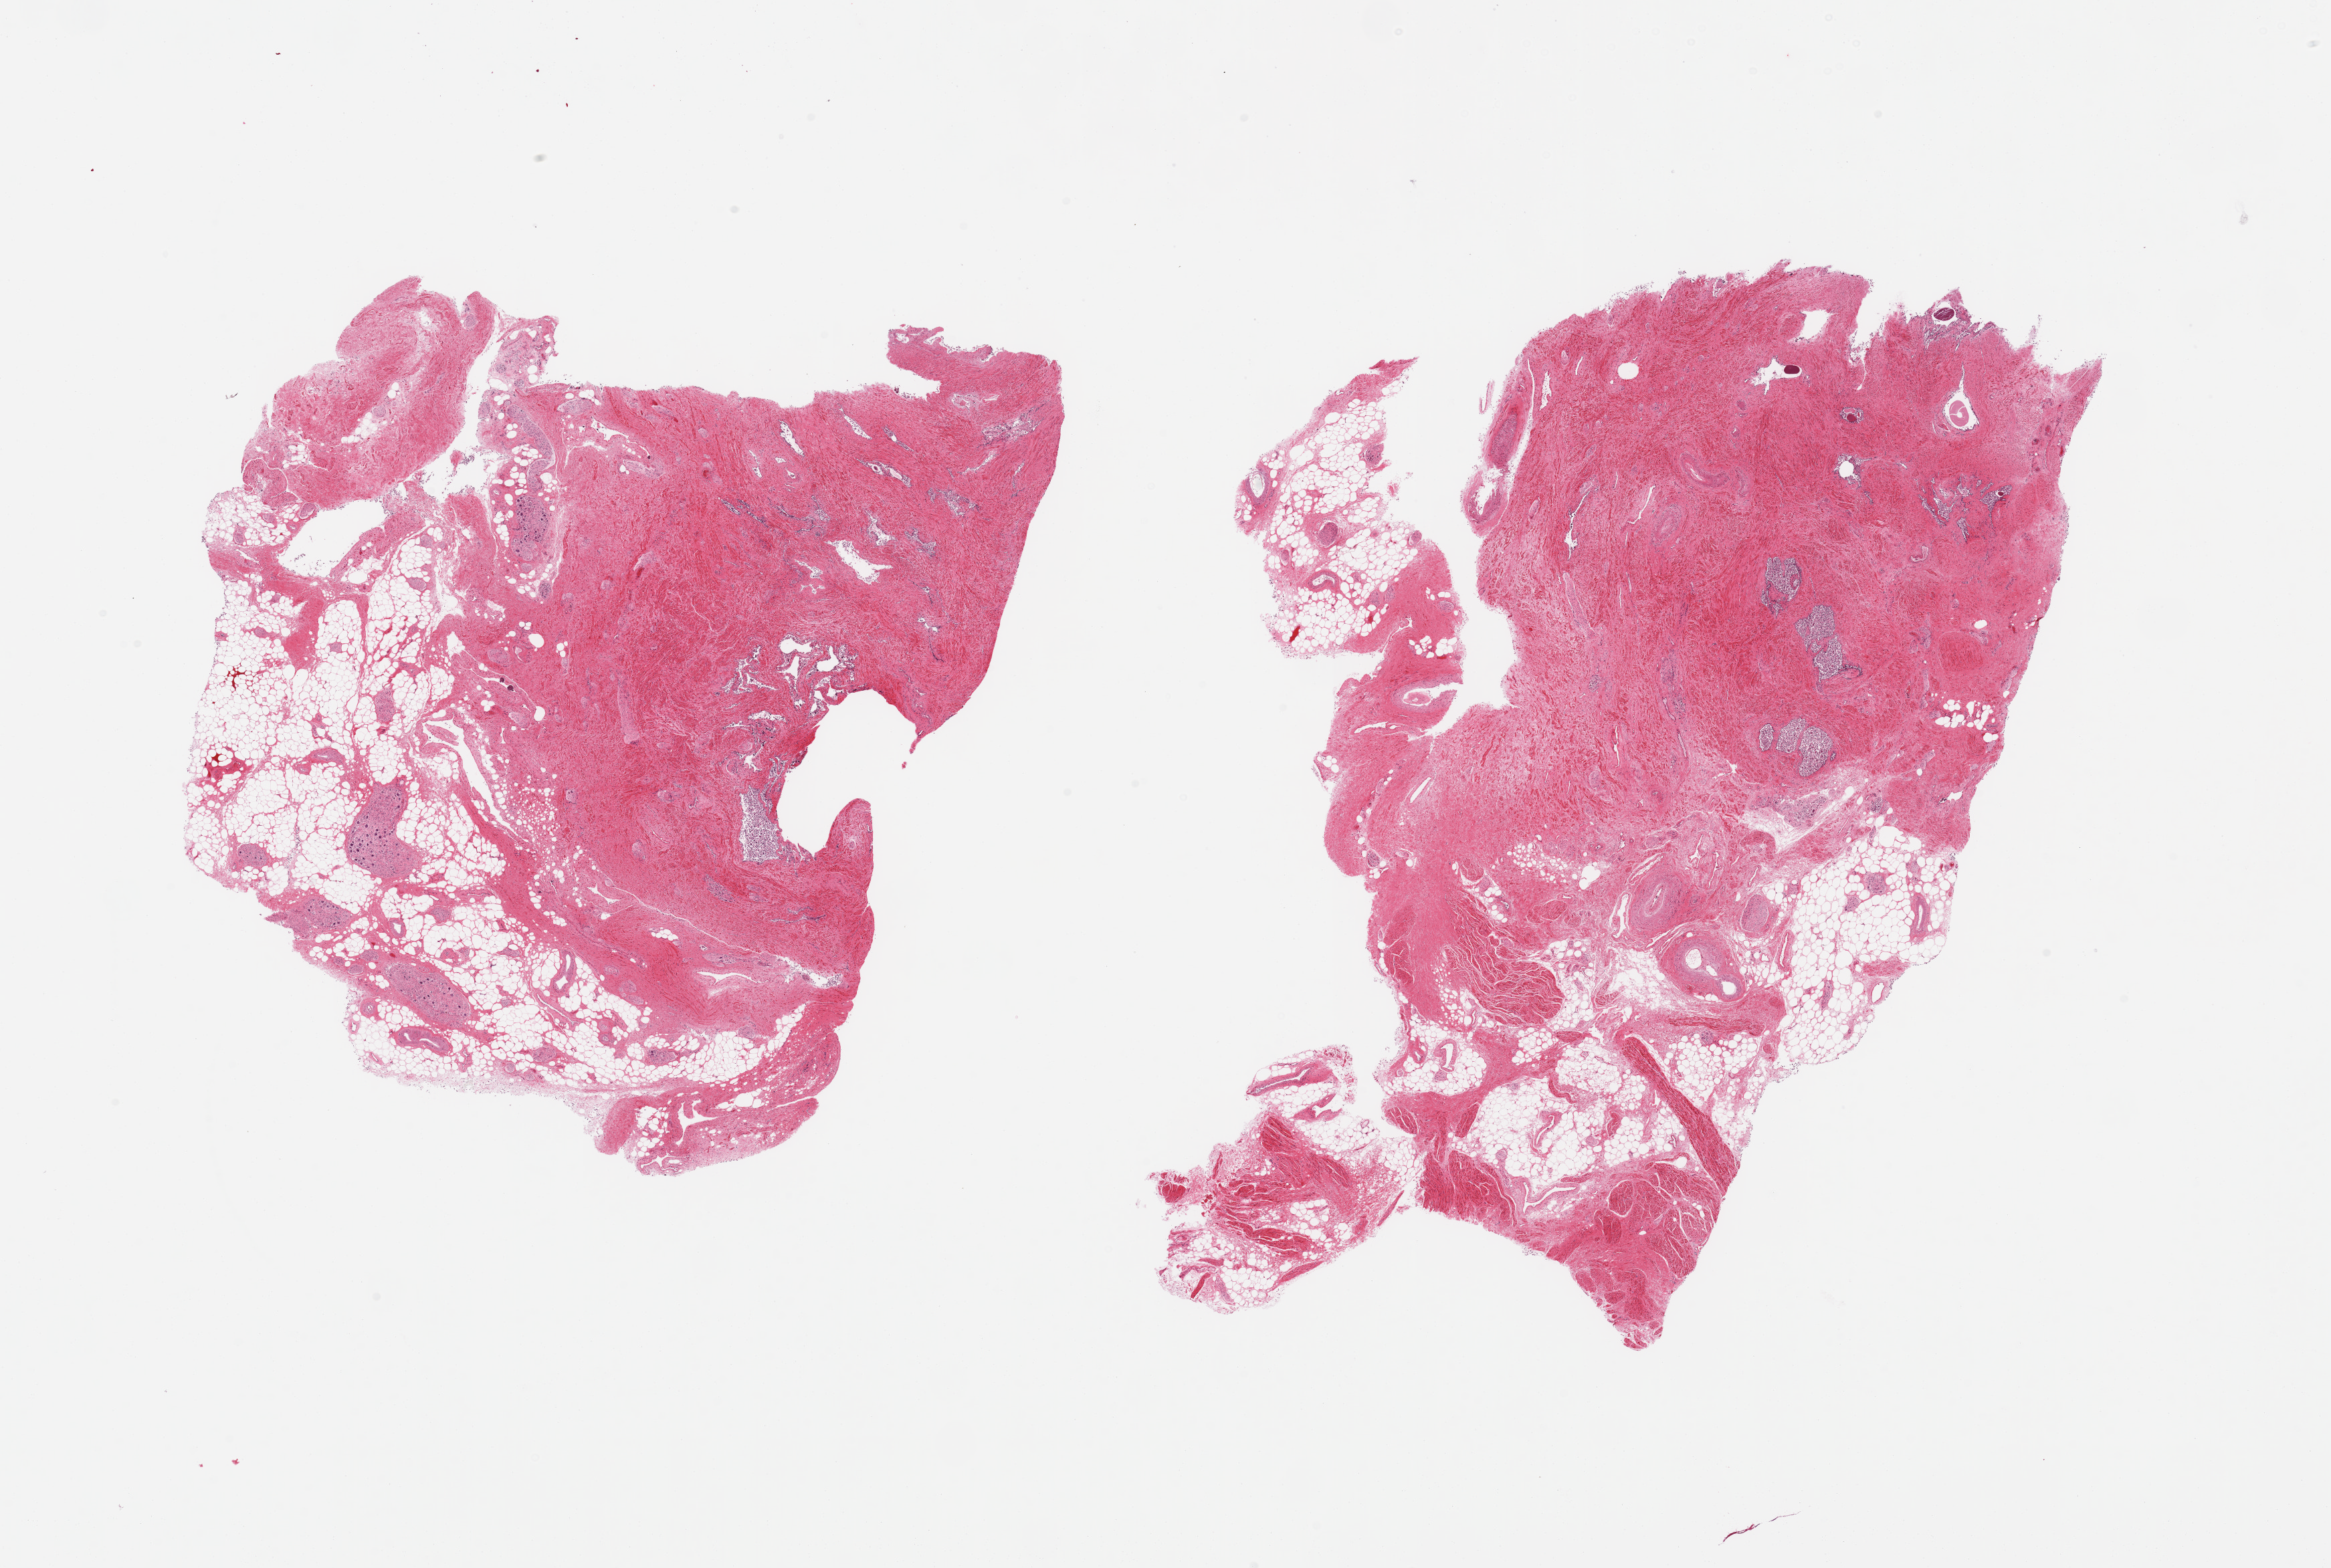
Whole-slide image, haematoxylin and eosin stain, brightfield, a low-resolution overview of the entire scanned area, about 27.6 x 18.5 mm, PAXgene-fixed paraffin-embedded (PFPE) section, sampled site (target tissue): prostate, tissue donor sample. Male donor.
• pathologist's review note for this sample: 2 pieces, glandular elements with markedly advanced autolysis, stroma fairly well preserved